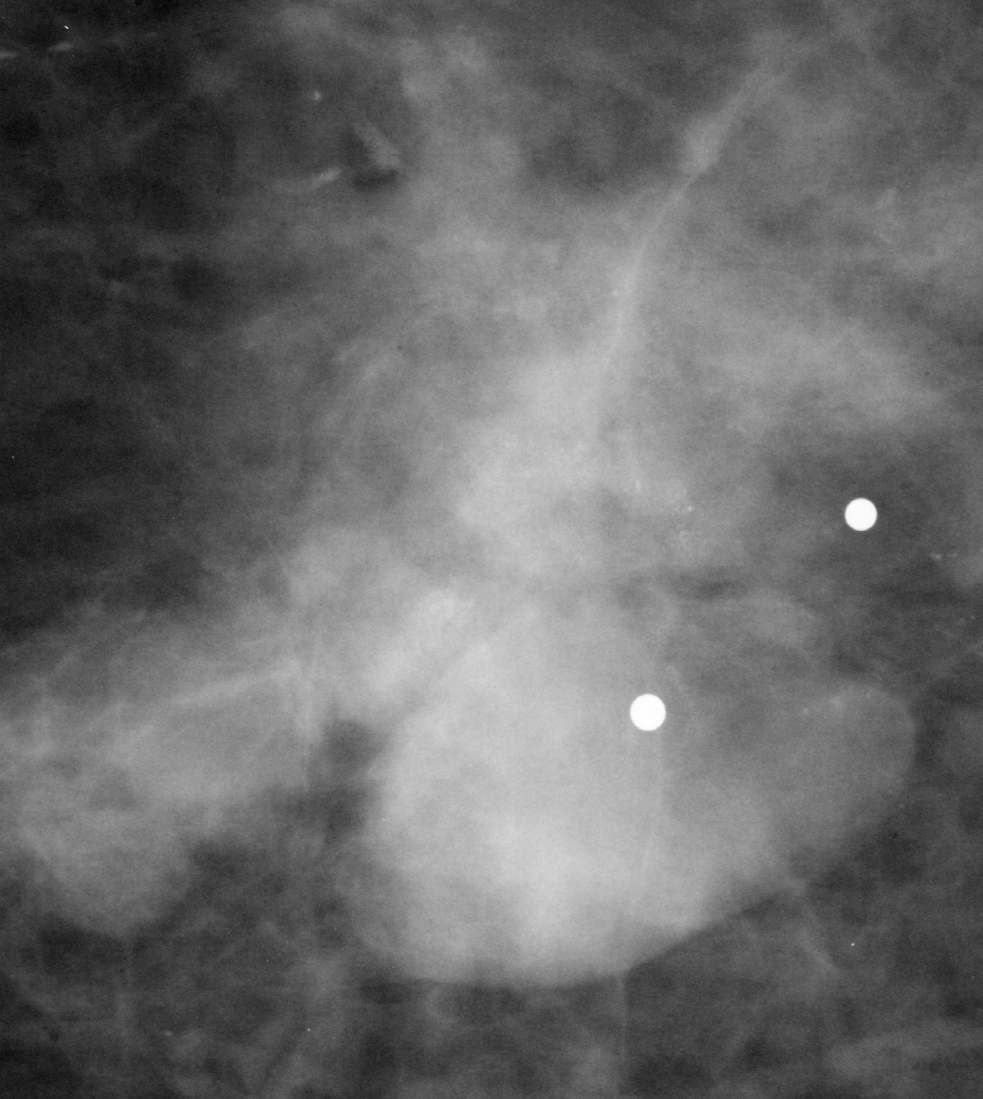
Cropped region of a digitized screen-film mammogram centred on a radiologist-marked abnormality, left breast, CC view, BI-RADS breast density category 2 (scale 1–4).
Marked abnormality: mass, shape irregular, margins spiculated; BI-RADS assessment category 5; pathology (as recorded): malignant.